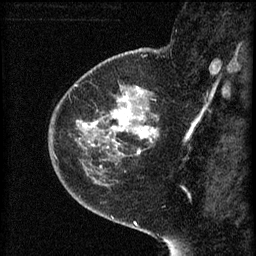
Breast MRI (dynamic contrast-enhanced), one sagittal slice; position 18 of 60 along the scan axis; 3 images stored at this slice position (order not interpretable as contrast timing); 1.5 T; TE 4.2 ms, TR 8.2 ms; 2 mm slice thickness; 256 × 256 image matrix, field of view 180 × 180 mm. Patient: female, 44 years.
Structures marked on this image (semi-automatically segmented with operator editing):
- analysis volume of interest (the breast-tissue region the enhancement analysis was run in; not a lesion): bounding box (x1, y1, x2, y2) in pixels: (73, 82, 161, 165)
- tumour enhancement mask (voxels above the 70 % enhancement threshold inside the analysis volume of interest): (77, 88, 159, 155)